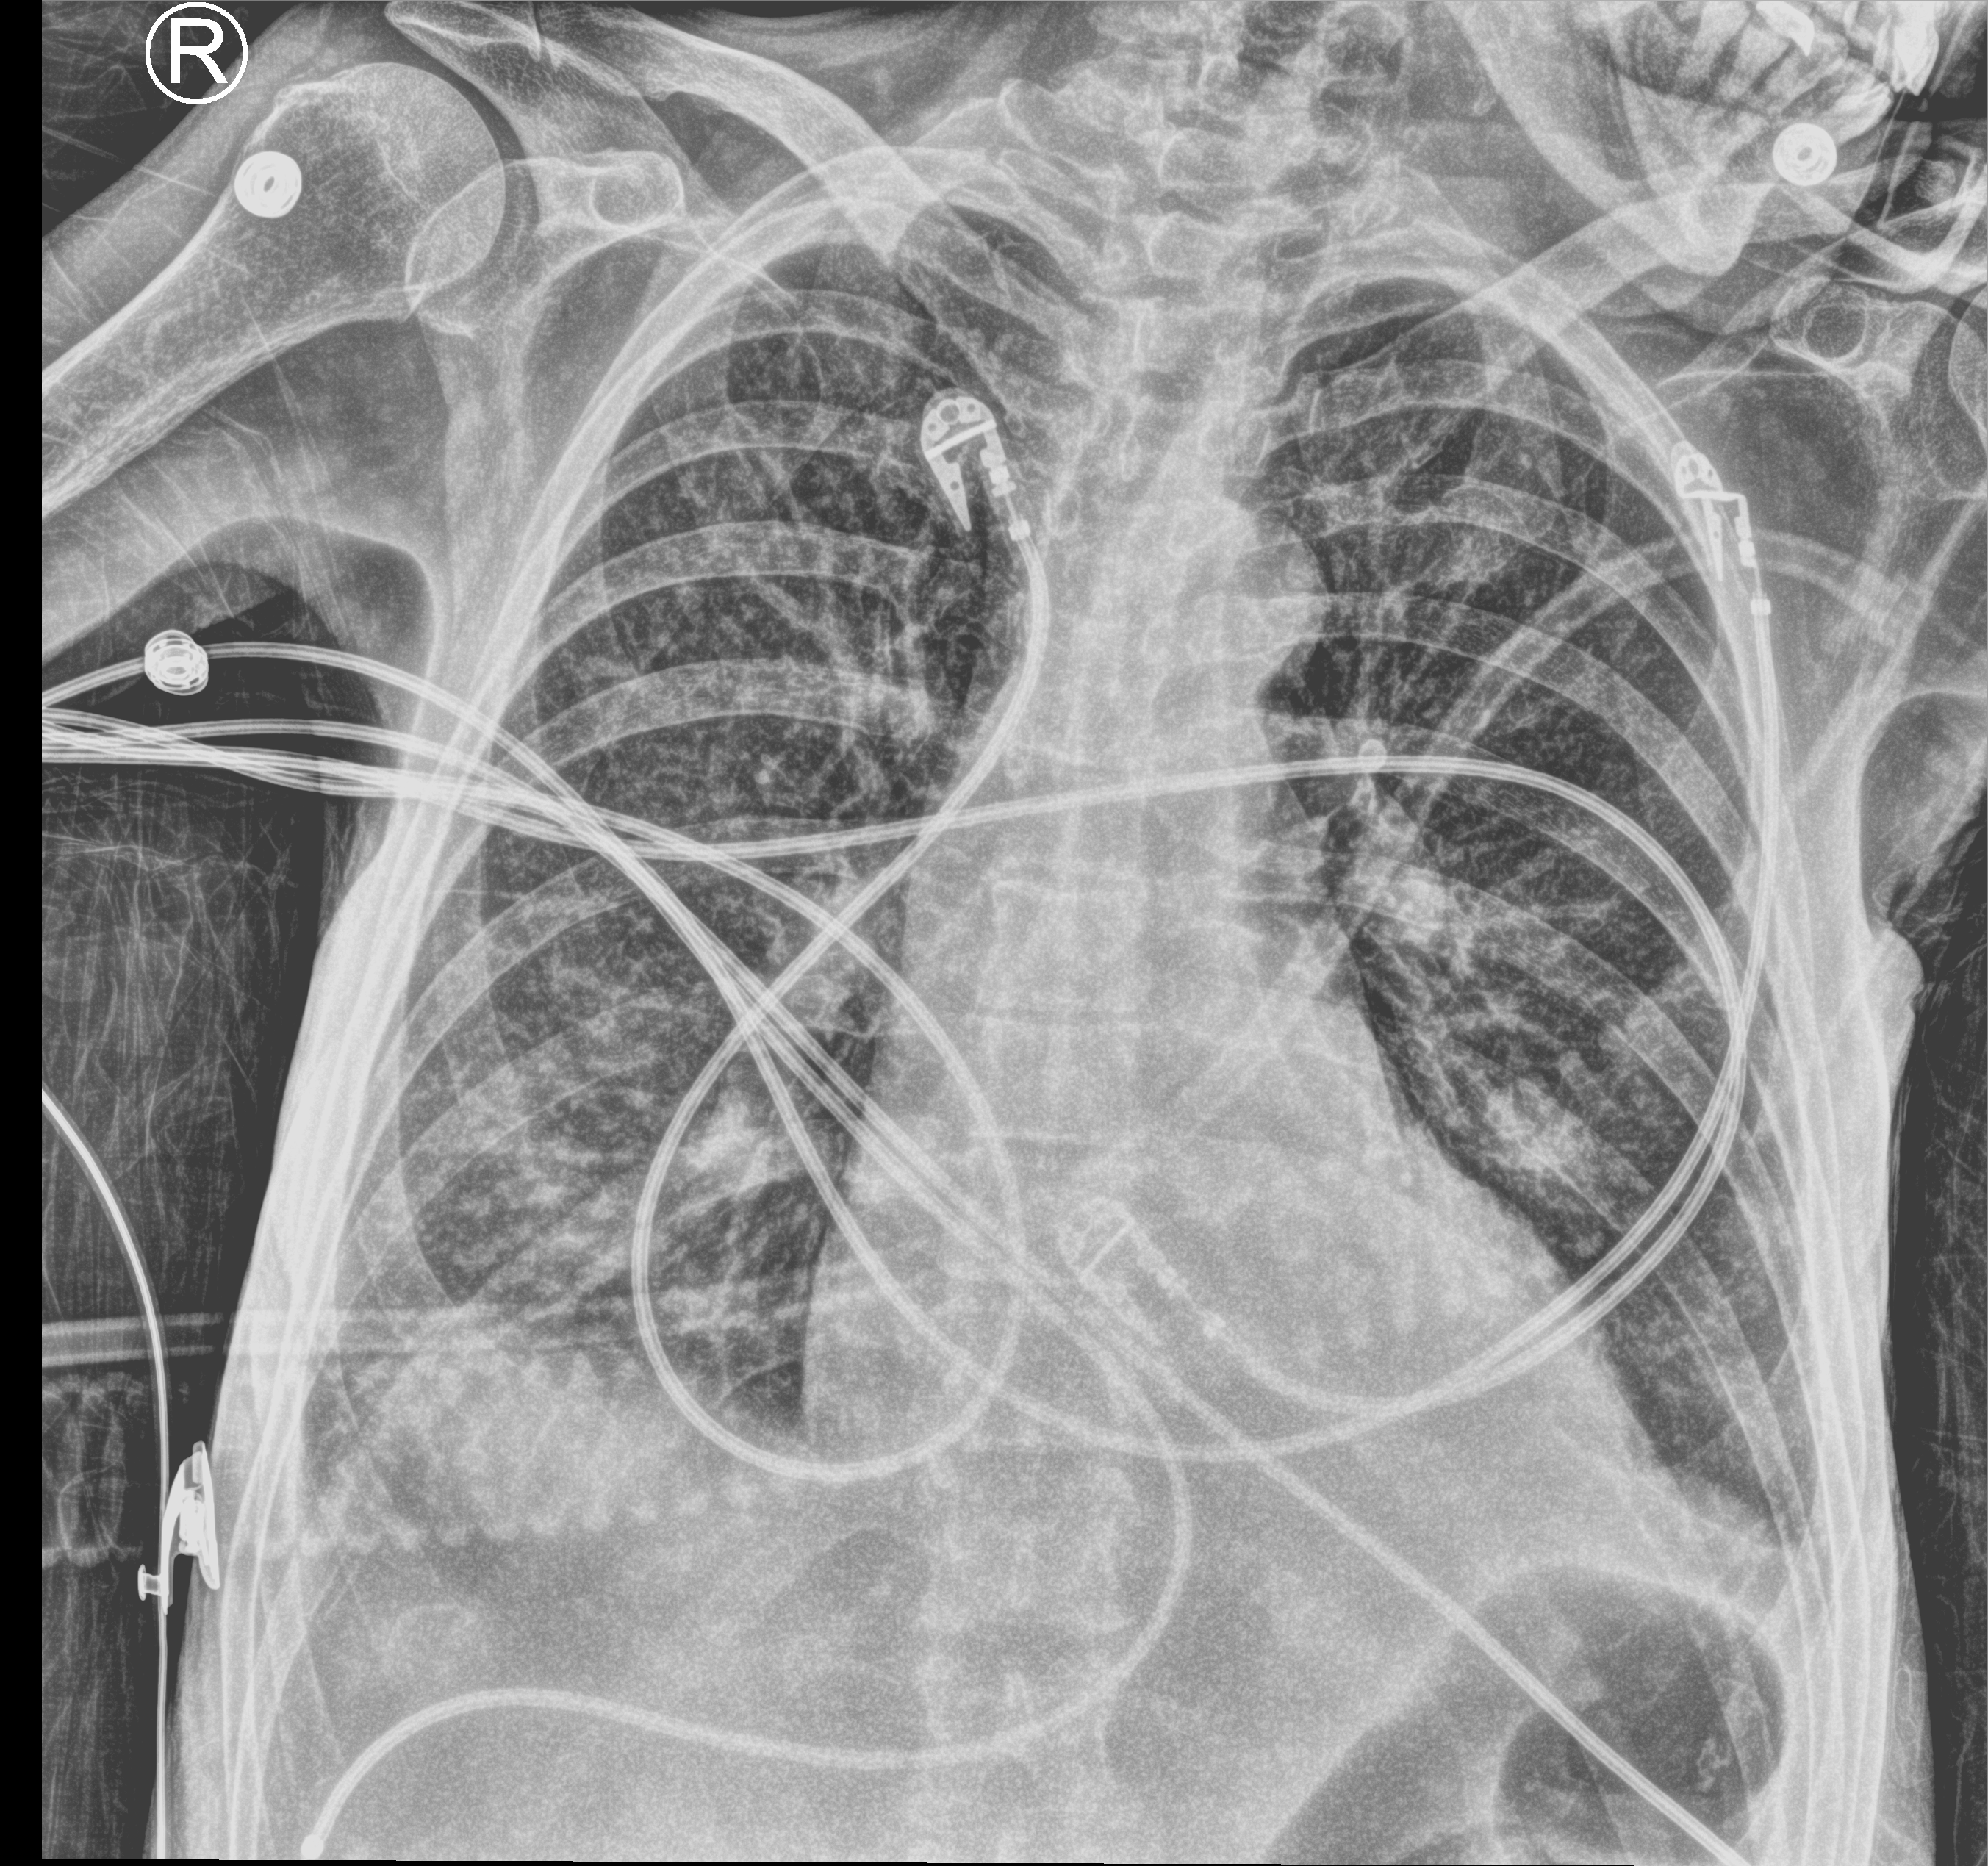
Portable chest radiograph; anteroposterior (AP) projection. Patient hospitalised with COVID-19; female, aged 60–74 years.
Hospital-stay facts (about this admission, not read from this image; timing relative to this image not recorded):
- mechanically ventilated during this hospital stay: yes